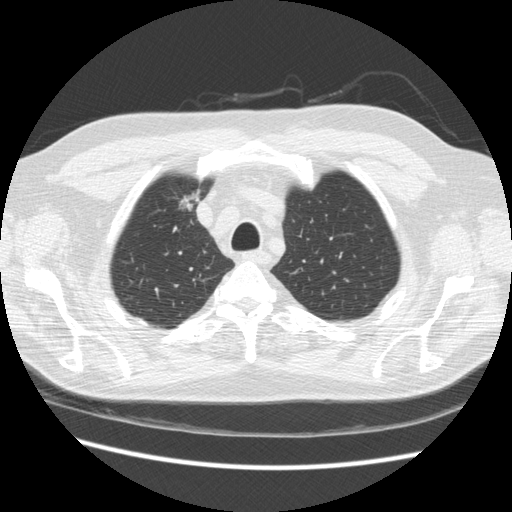
Low-dose screening chest CT, one axial slice; slice 189 of 234 in the series (ordered by position); reconstruction kernel STANDARD; 120 kVp; lung window (W 1500 / L -600 HU); 2.5 mm slice thickness; 512 × 512 image matrix, field of view 360 × 360 mm.
Annotated regions visible in this slice (outlined manually by an expert reader):
- lesion 1 (tumor, upper lobe of right lung): bounding box [x1, y1, x2, y2] px = [178, 190, 201, 211]